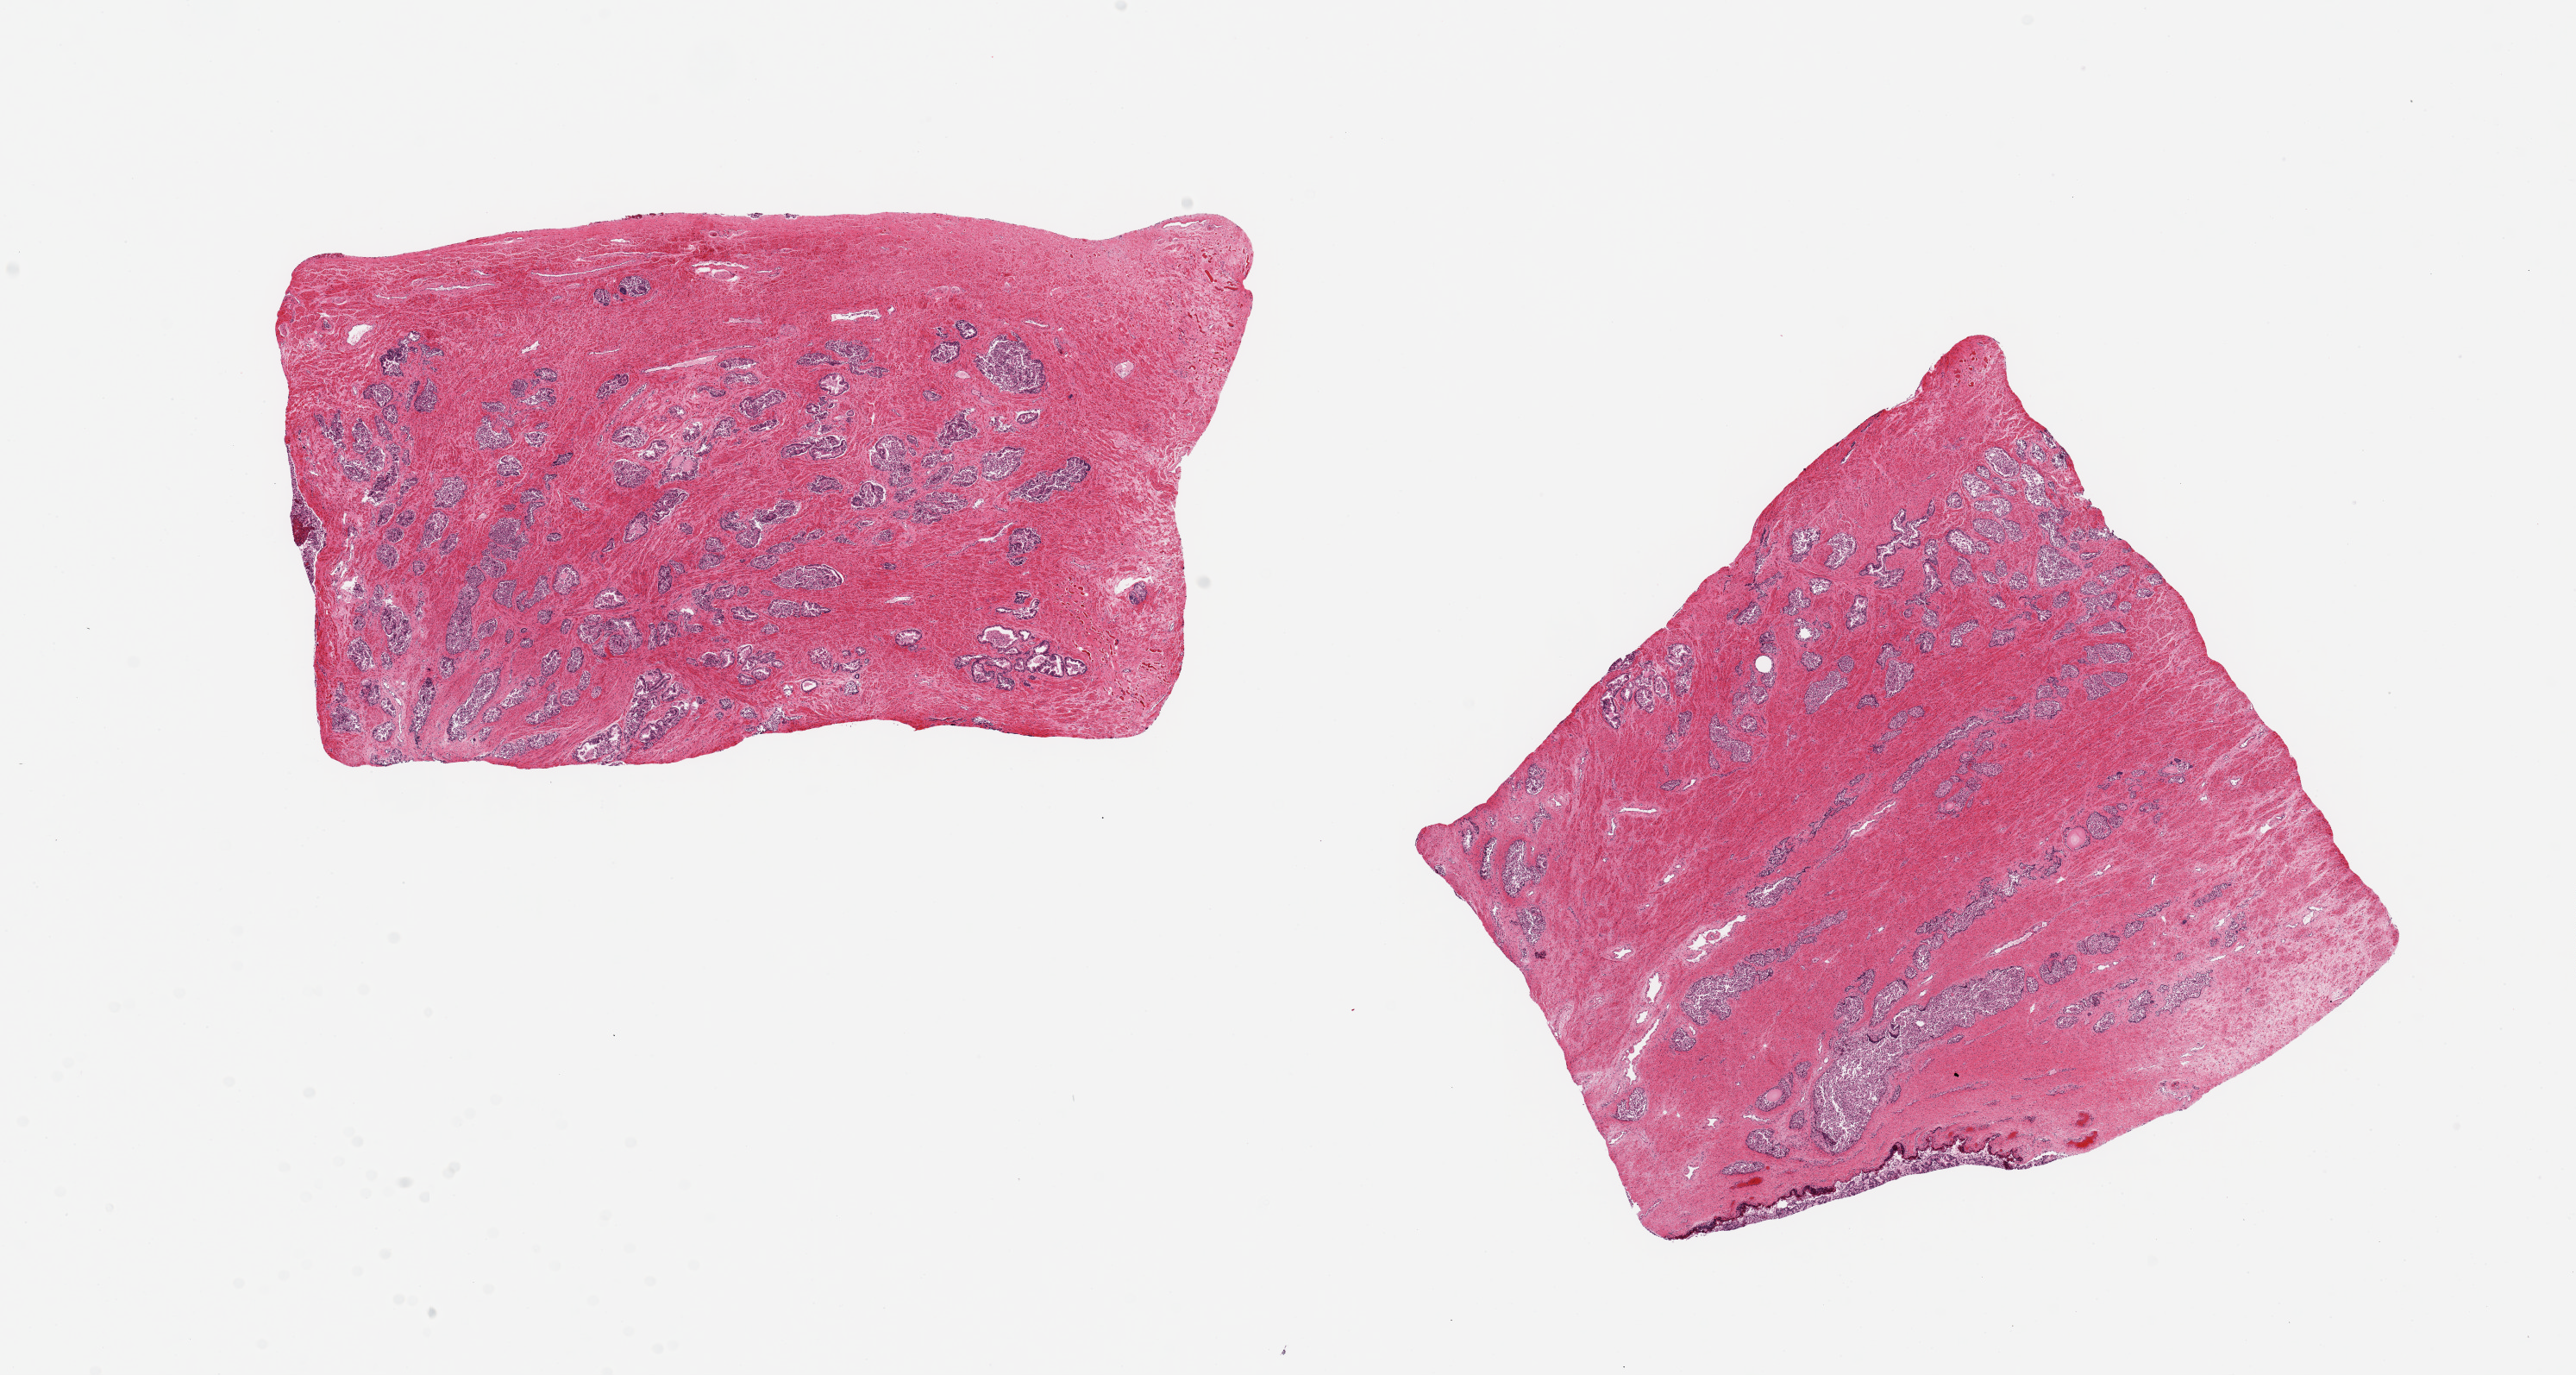
H&E whole-slide image — low-resolution overview of the scanned area, about 23.6 x 12.6 mm (from a 20x scan). PAXgene-fixed, paraffin-embedded tissue. Sampled site (target tissue): prostate. Tissue donor sample. Donor sex: male.
Pathologist's review note for this sample: 2 pieces ~7x6mm. Glands badly autolyzed.